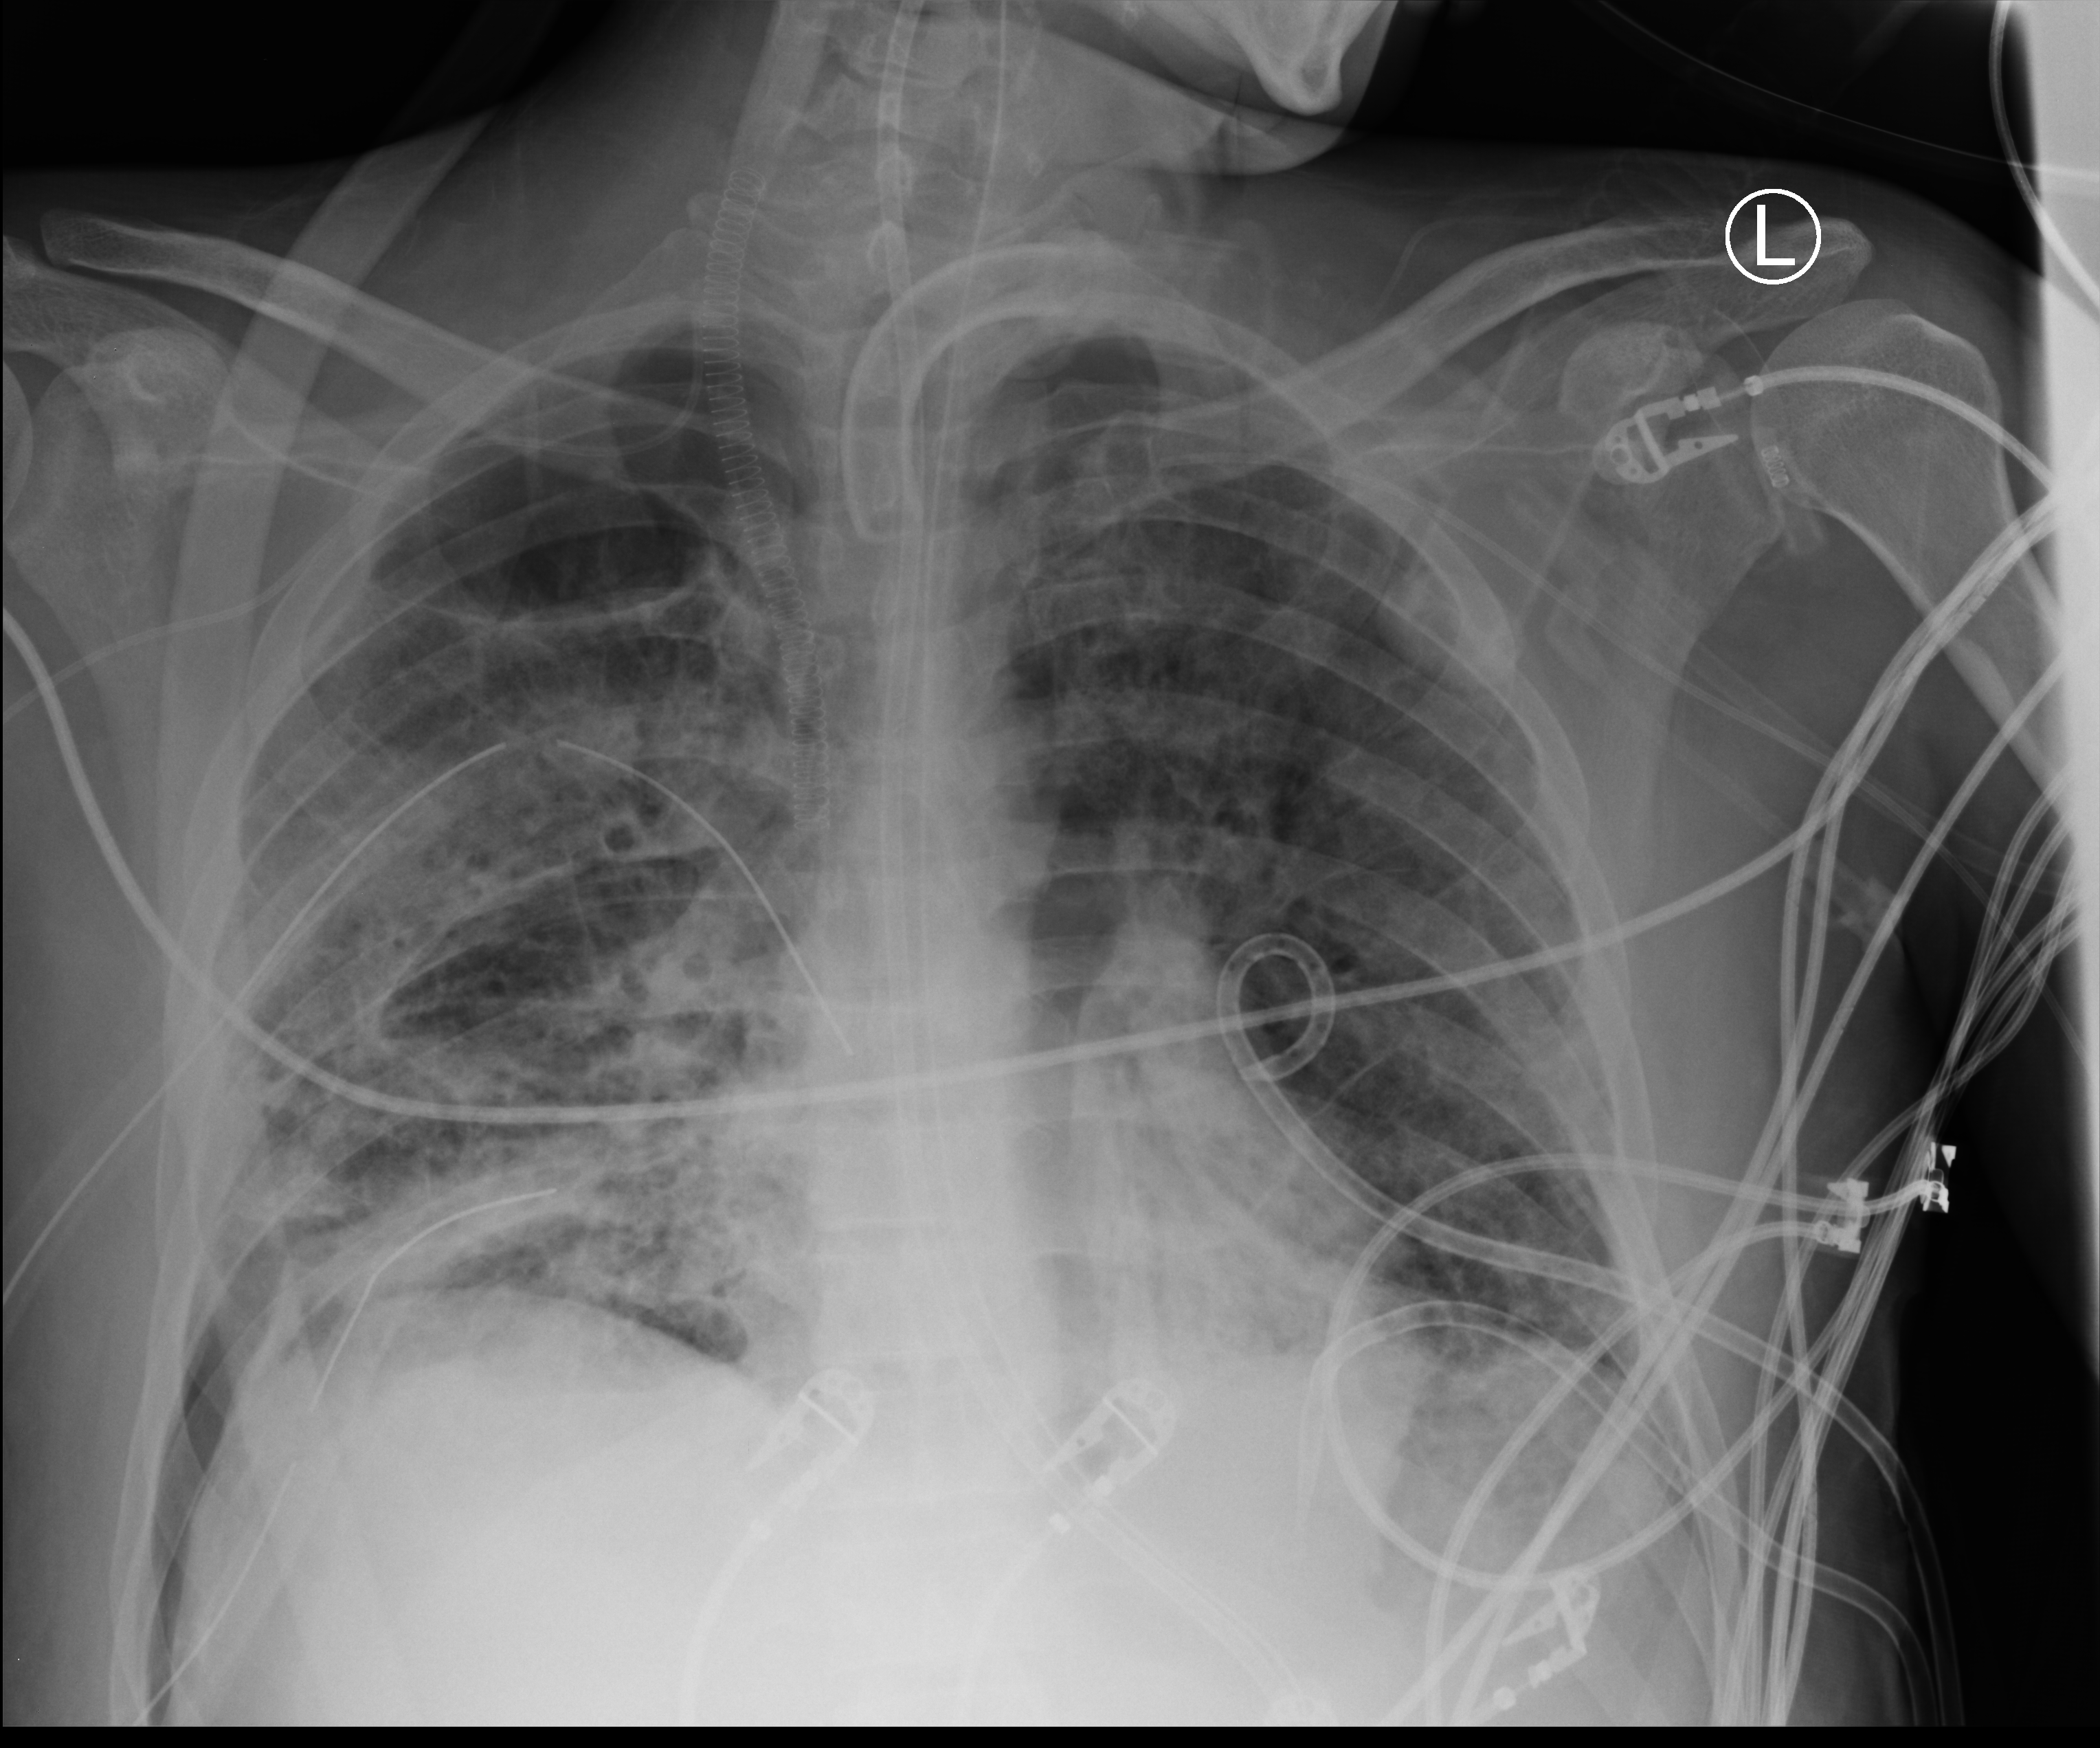
Bedside chest radiograph (computed radiography). Adult patient hospitalised with COVID-19, age 18–59 years.
Admission-level facts for this patient (not findings on this image; timing relative to this image not recorded):
- smoking status (admission record): never
- admitted to intensive care during this hospital stay: yes